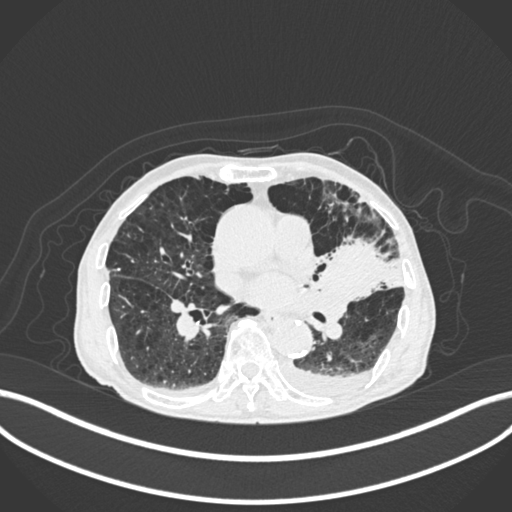
Chest CT, one axial slice. Reconstruction kernel B30f. Lung window (W 1500 / L -600 HU). 1 mm slice thickness. 512 × 512 image matrix. Patient: male, 90 years or older. Case-level facts recorded for this patient, not image findings: clinical TNM (as recorded): T2b N1 M0.
Structures marked on this image (rectangle marked by the reading radiologist):
- lung tumour (recorded histology: squamous cell carcinoma): bounding box <312,236,386,303> (left, top, right, bottom; pixels)